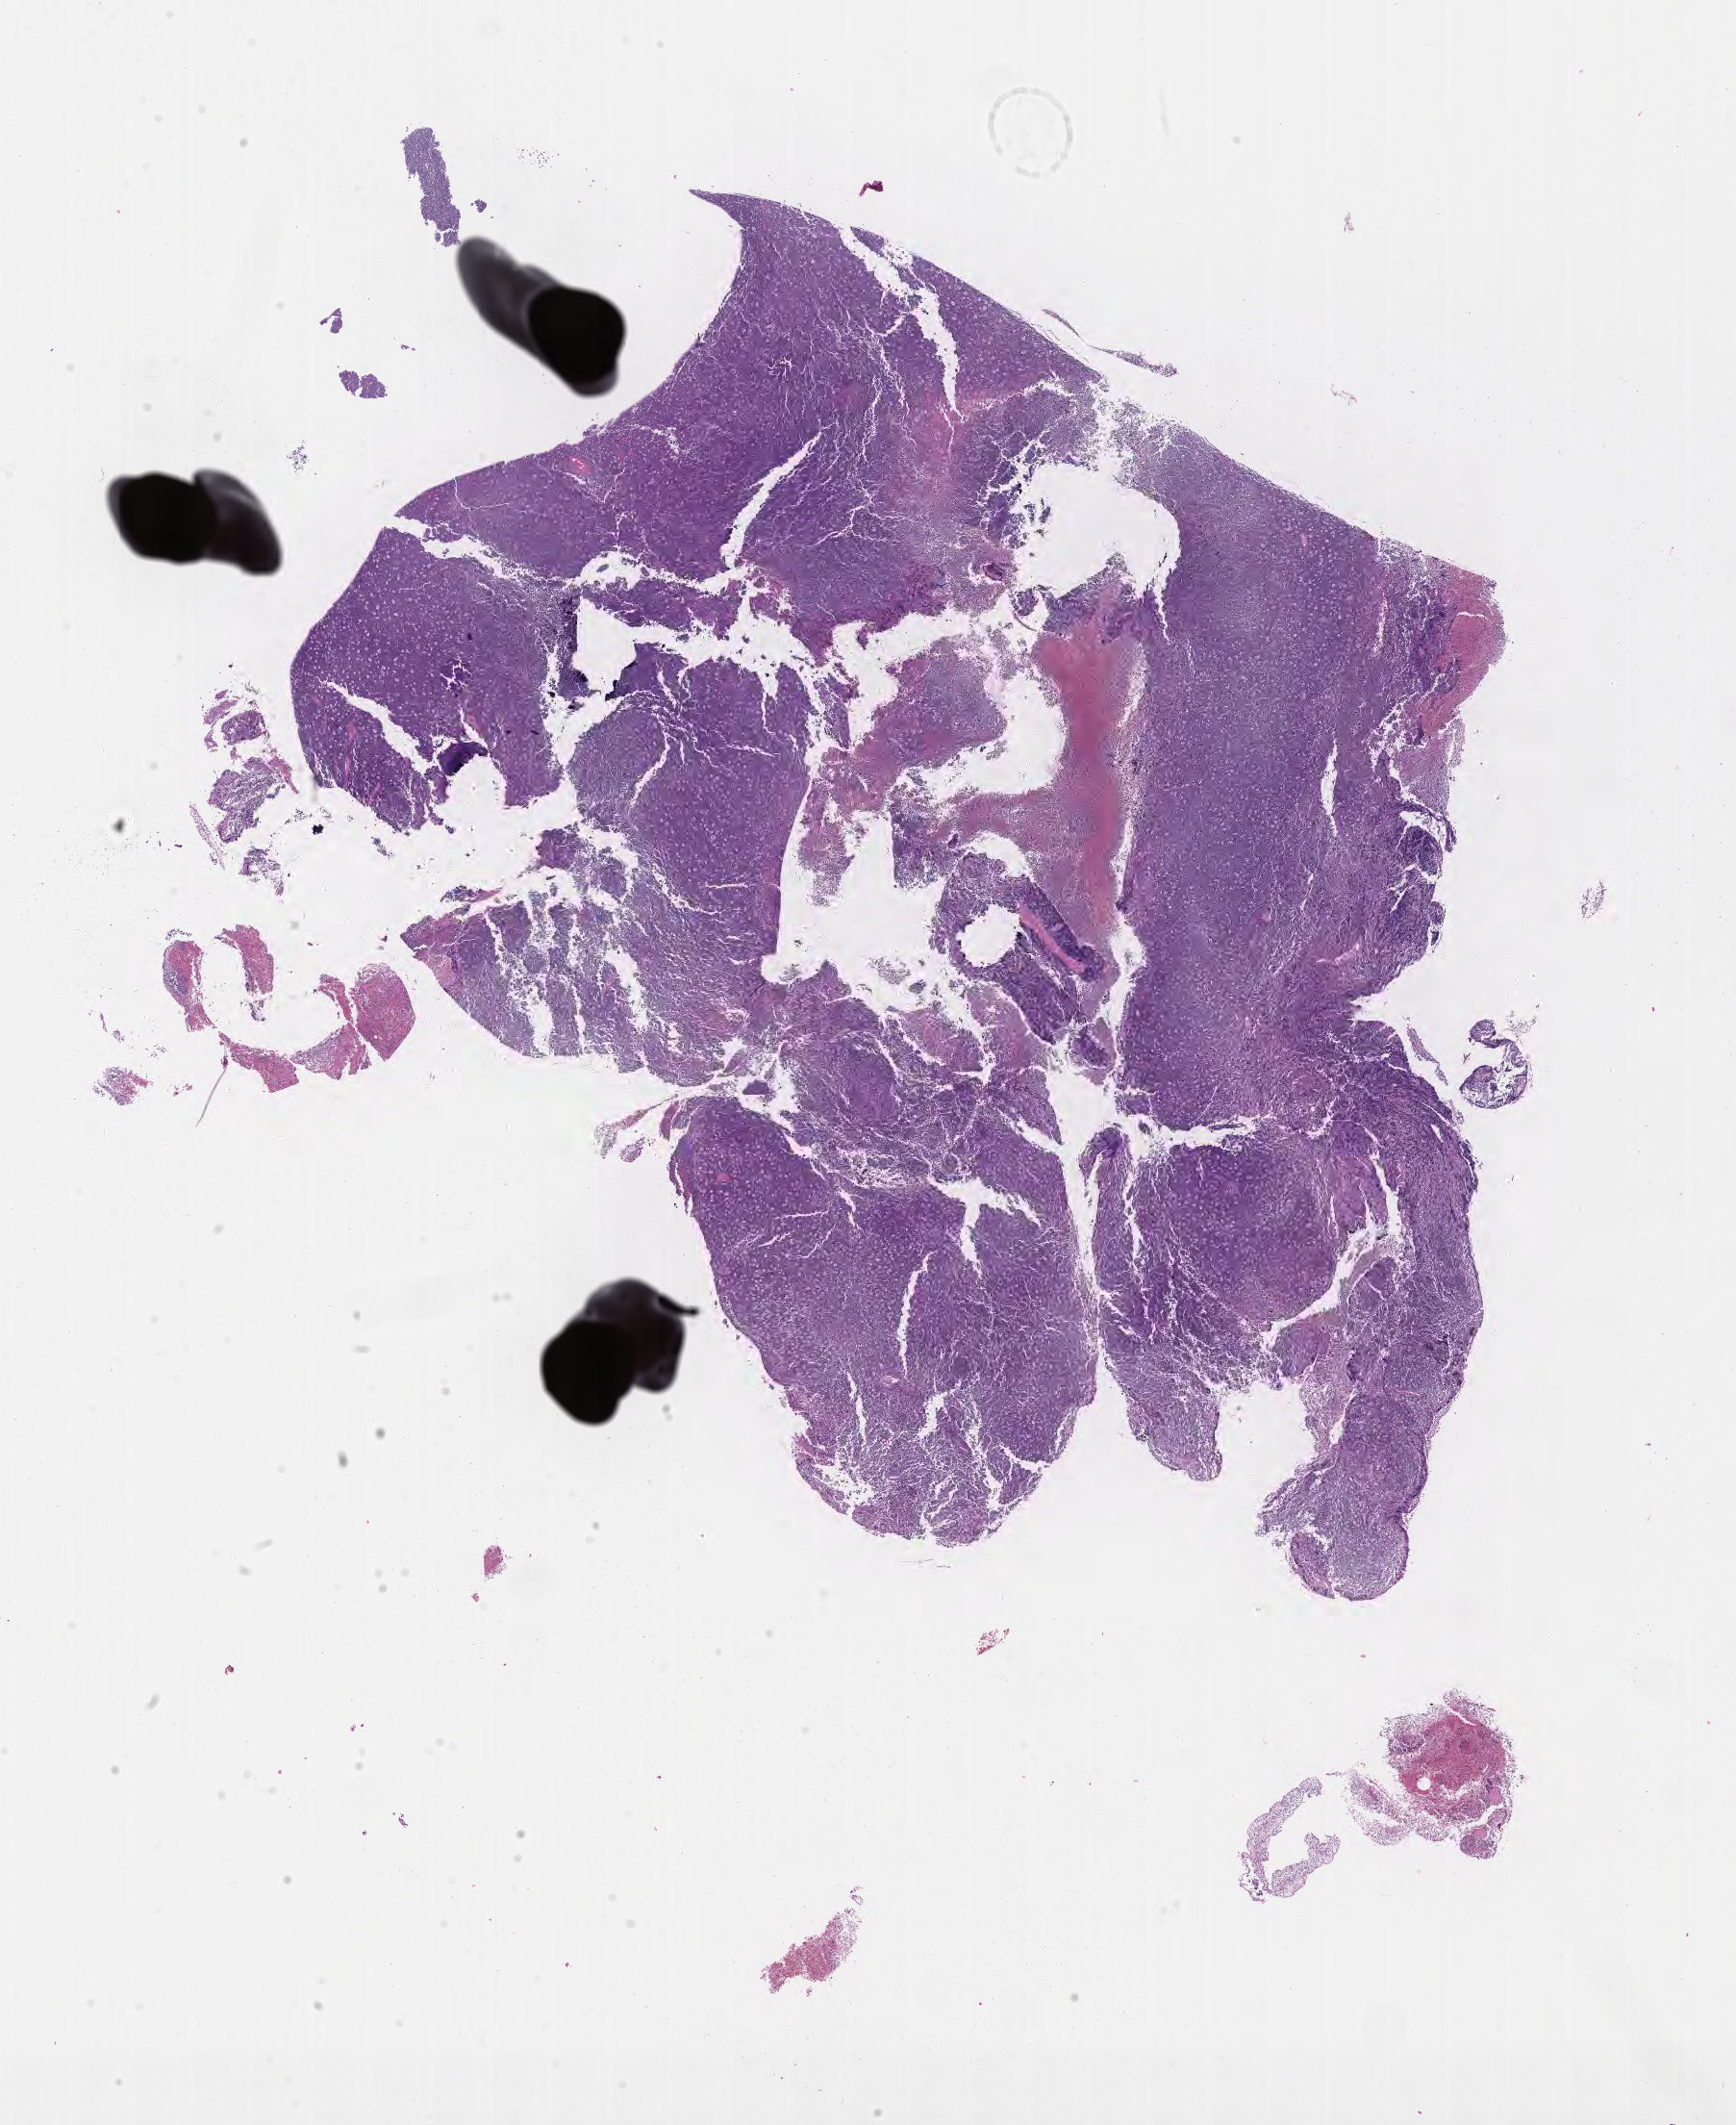
Digitized H&E-stained section — whole scanned area (about 14.6 x 17.9 mm) shown as a low-resolution overview. Patient male; 51 years old.
Specimen: tumor tissue.